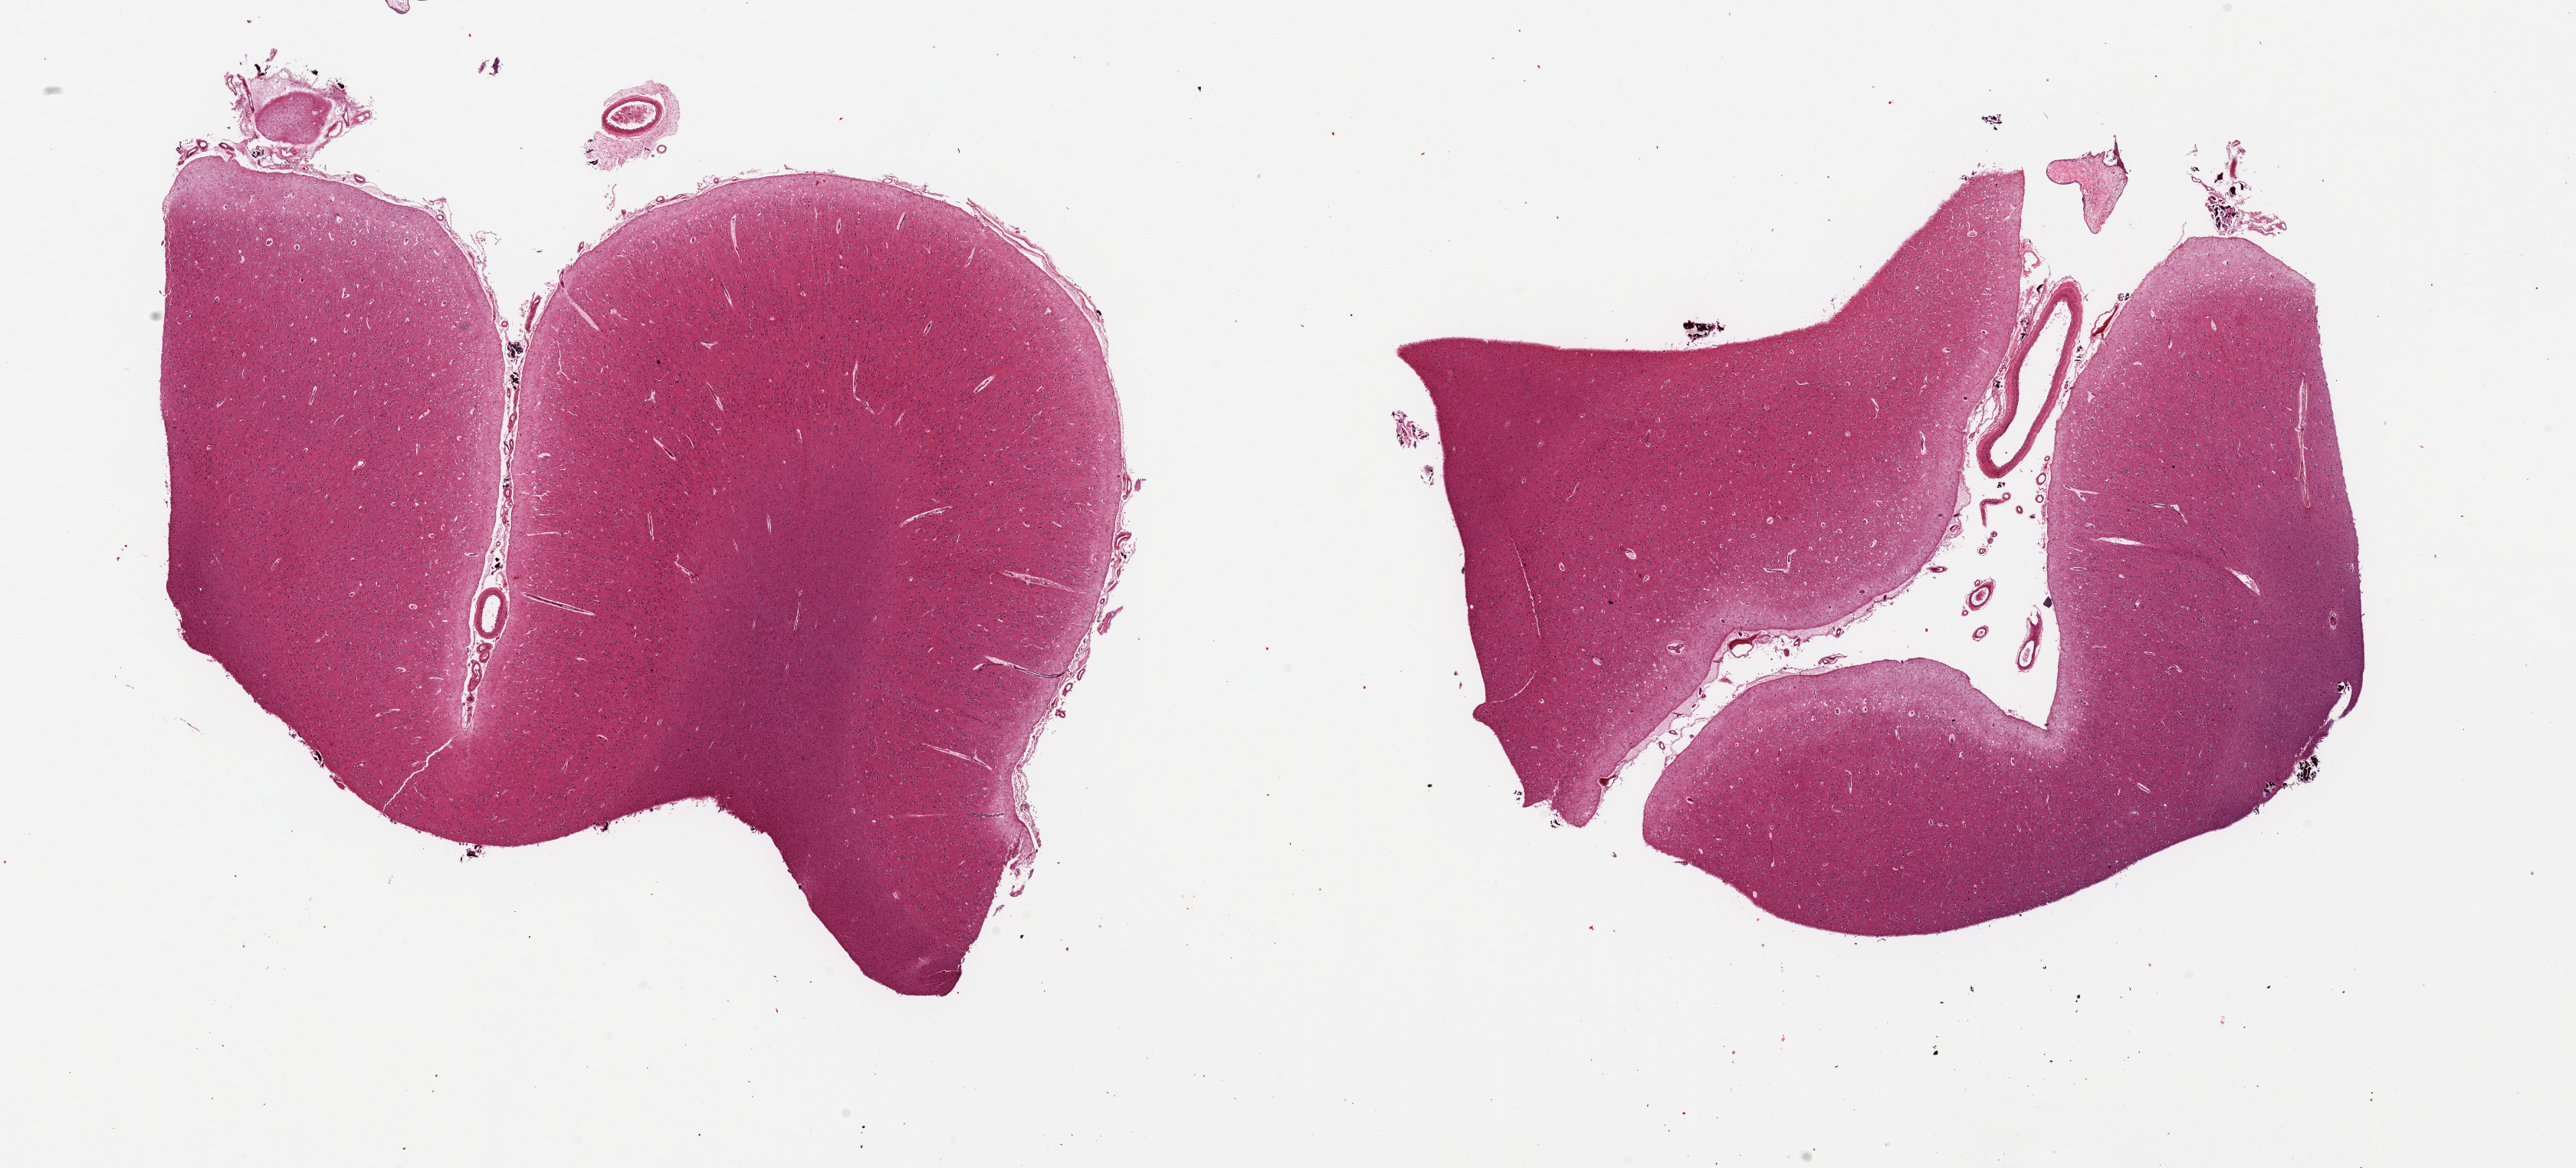
H&E whole-slide image — shown as a low-resolution overview of the whole scanned area (about 26.6 x 12.1 mm, from a 20x scan). PAXgene-fixed, paraffin-embedded tissue. Section of cerebral cortex (target tissue). Tissue donor sample. Donor: female.
Review note (as recorded): 2 pieces.